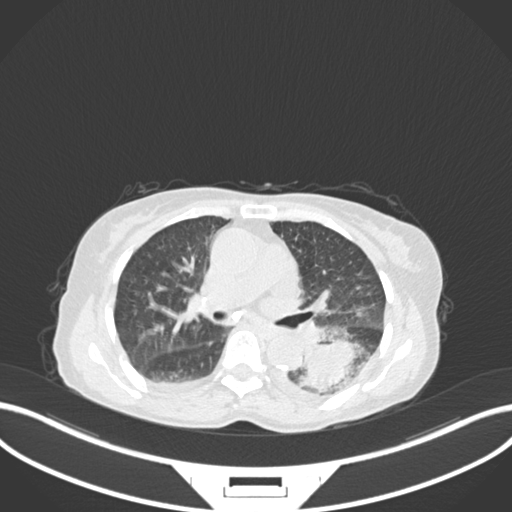
Chest CT, one axial slice; slice 100 of 233 in the series (ordered by position); reconstruction kernel B30f; lung window (W 1500 / L -600 HU); 1 mm slice thickness; 512 × 512 image matrix. Patient: female, 78 years. From the clinical record (not read from this slice): clinical TNM (as recorded): T3 N0 M1.
Annotated regions visible in this slice (bounding box drawn by a radiologist):
- lung tumour (recorded histology: squamous cell carcinoma): box from (x=294, y=336) to (x=371, y=396) px